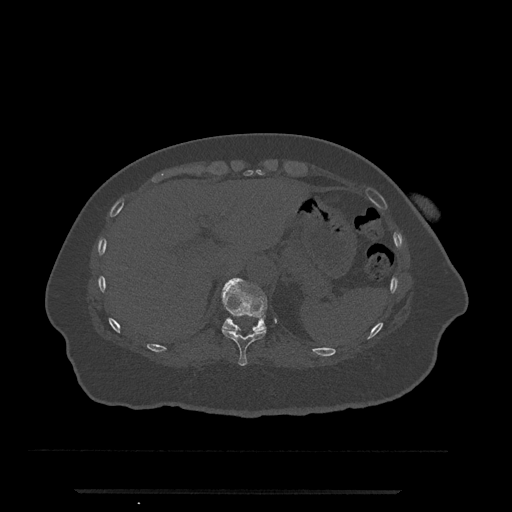
CT including the spine, one axial slice; position 261 of 797 along the scan axis; 120 kVp; bone window (W 1800 / L 400 HU); 0.5 mm slice thickness; 512 × 512 image matrix, field of view 440 × 440 mm. Patient: female, 51 years. From the clinical record (not read from this slice): primary cancer: neuro.
Structures marked on this image (semi-automatically segmented with operator editing):
- T10 vertebra: bounding box (x1, y1, x2, y2) in pixels: (222, 327, 267, 366)
- T11 vertebra: (222, 278, 267, 333)